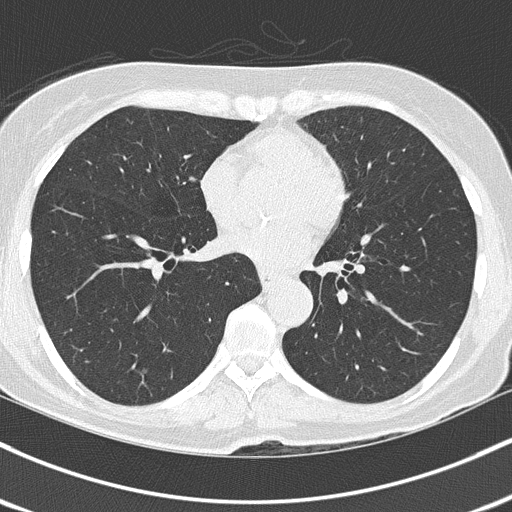
Chest CT (low-dose screening protocol), one axial image; baseline annual screen; lung window (W 1500 / L -600 HU); 2 mm slice thickness; 120 kVp. Female, age 67 years at enrolment. Current smoker at enrolment.
Lesion marked by an expert reader, box from (x=134, y=360) to (x=158, y=380) px. Screening reader's record for this exam (one nodule recorded; not confirmed to be the boxed lesion): non-calcified nodule or mass ≥4 mm, left lower lobe, 7 × 6 mm, poorly defined margins, mixed attenuation. Note: the box lies in the patient's right hemithorax on this image, whereas the reader's record names the left lung; they may be different findings. Later outcome: lung cancer diagnosed 876 days after this screen — adenocarcinoma, NOS, left lower lobe, poorly differentiated (G3), stage IA (AJCC 6th edition), 25 mm at pathology.